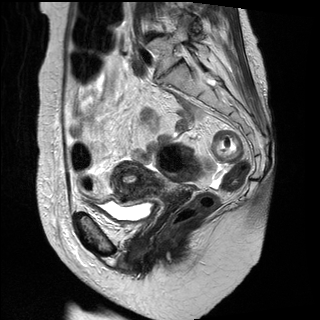
Pelvic MRI for cervical cancer, one sagittal slice; slice 18 of 31 in the series (ordered by position); T2-weighted; 1.5 T; TE 89 ms, TR 3890 ms; 4 mm slice thickness; 320 × 320 image matrix, field of view 260 × 260 mm. Patient: female, 61 years.
Outlined on this slice (outlined manually by an expert reader):
- uterus and cervix: box from (x=111, y=162) to (x=193, y=209) px